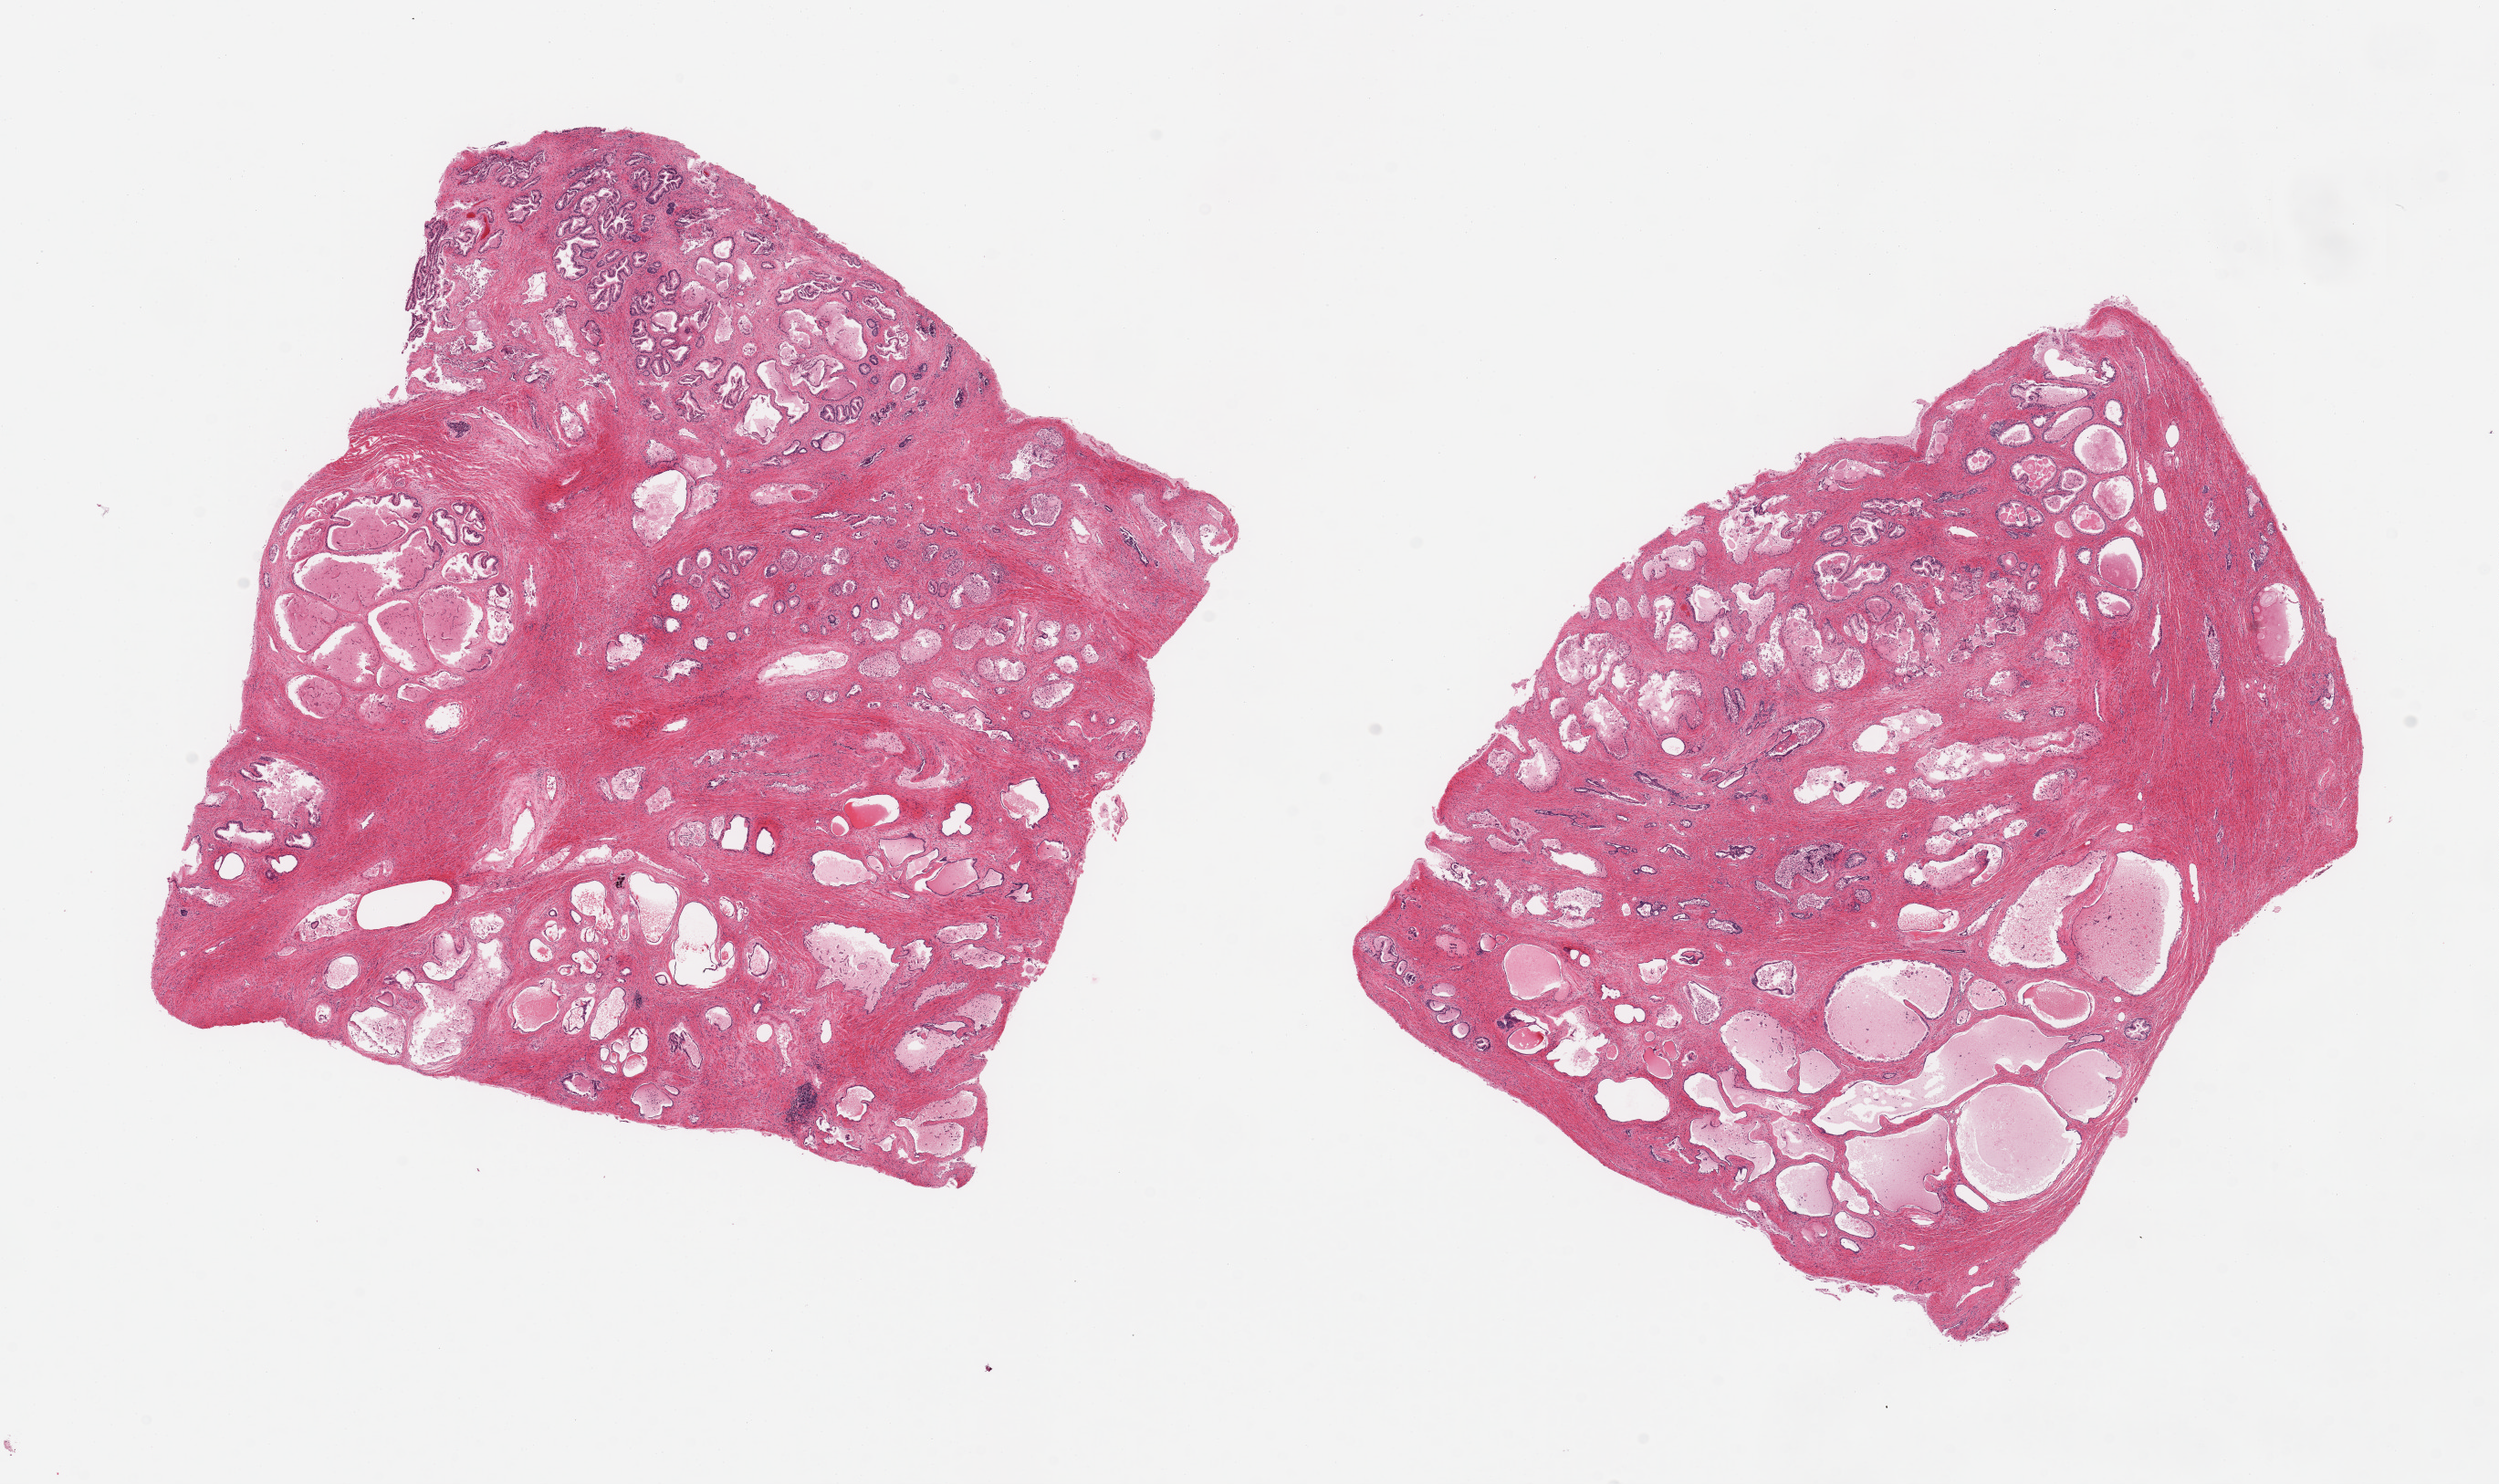
Whole-slide image, haematoxylin and eosin stain, brightfield, shown as a low-resolution overview of the whole scanned area (about 21.7 x 12.9 mm, acquisition: 20x scan), PAXgene-fixed paraffin-embedded (PFPE) section, sampled site (target tissue): prostate, donor tissue sample. Donor: male.
Reviewer comment on this tissue sample: 2 pieces, nodular hyperplastic pattern. Glandular preservation score ranges from 1 to 3.